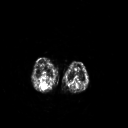
FDG PET of an extremity soft-tissue mass (from a PET/CT study), one axial slice. Position 162 of 267 along the scan axis. 3.27 mm slice thickness. 128 × 128 image matrix. Female patient, age 62 years. Case-level facts recorded for this patient, not image findings: histological type: liposarcoma; site of the primary tumour: right thigh.
Outlined on this slice (expert contour drawn on MRI and transferred to this co-registered scan by the dataset authors):
- gross tumour volume (mass): bounding box [x1, y1, x2, y2] px = [42, 84, 48, 89]